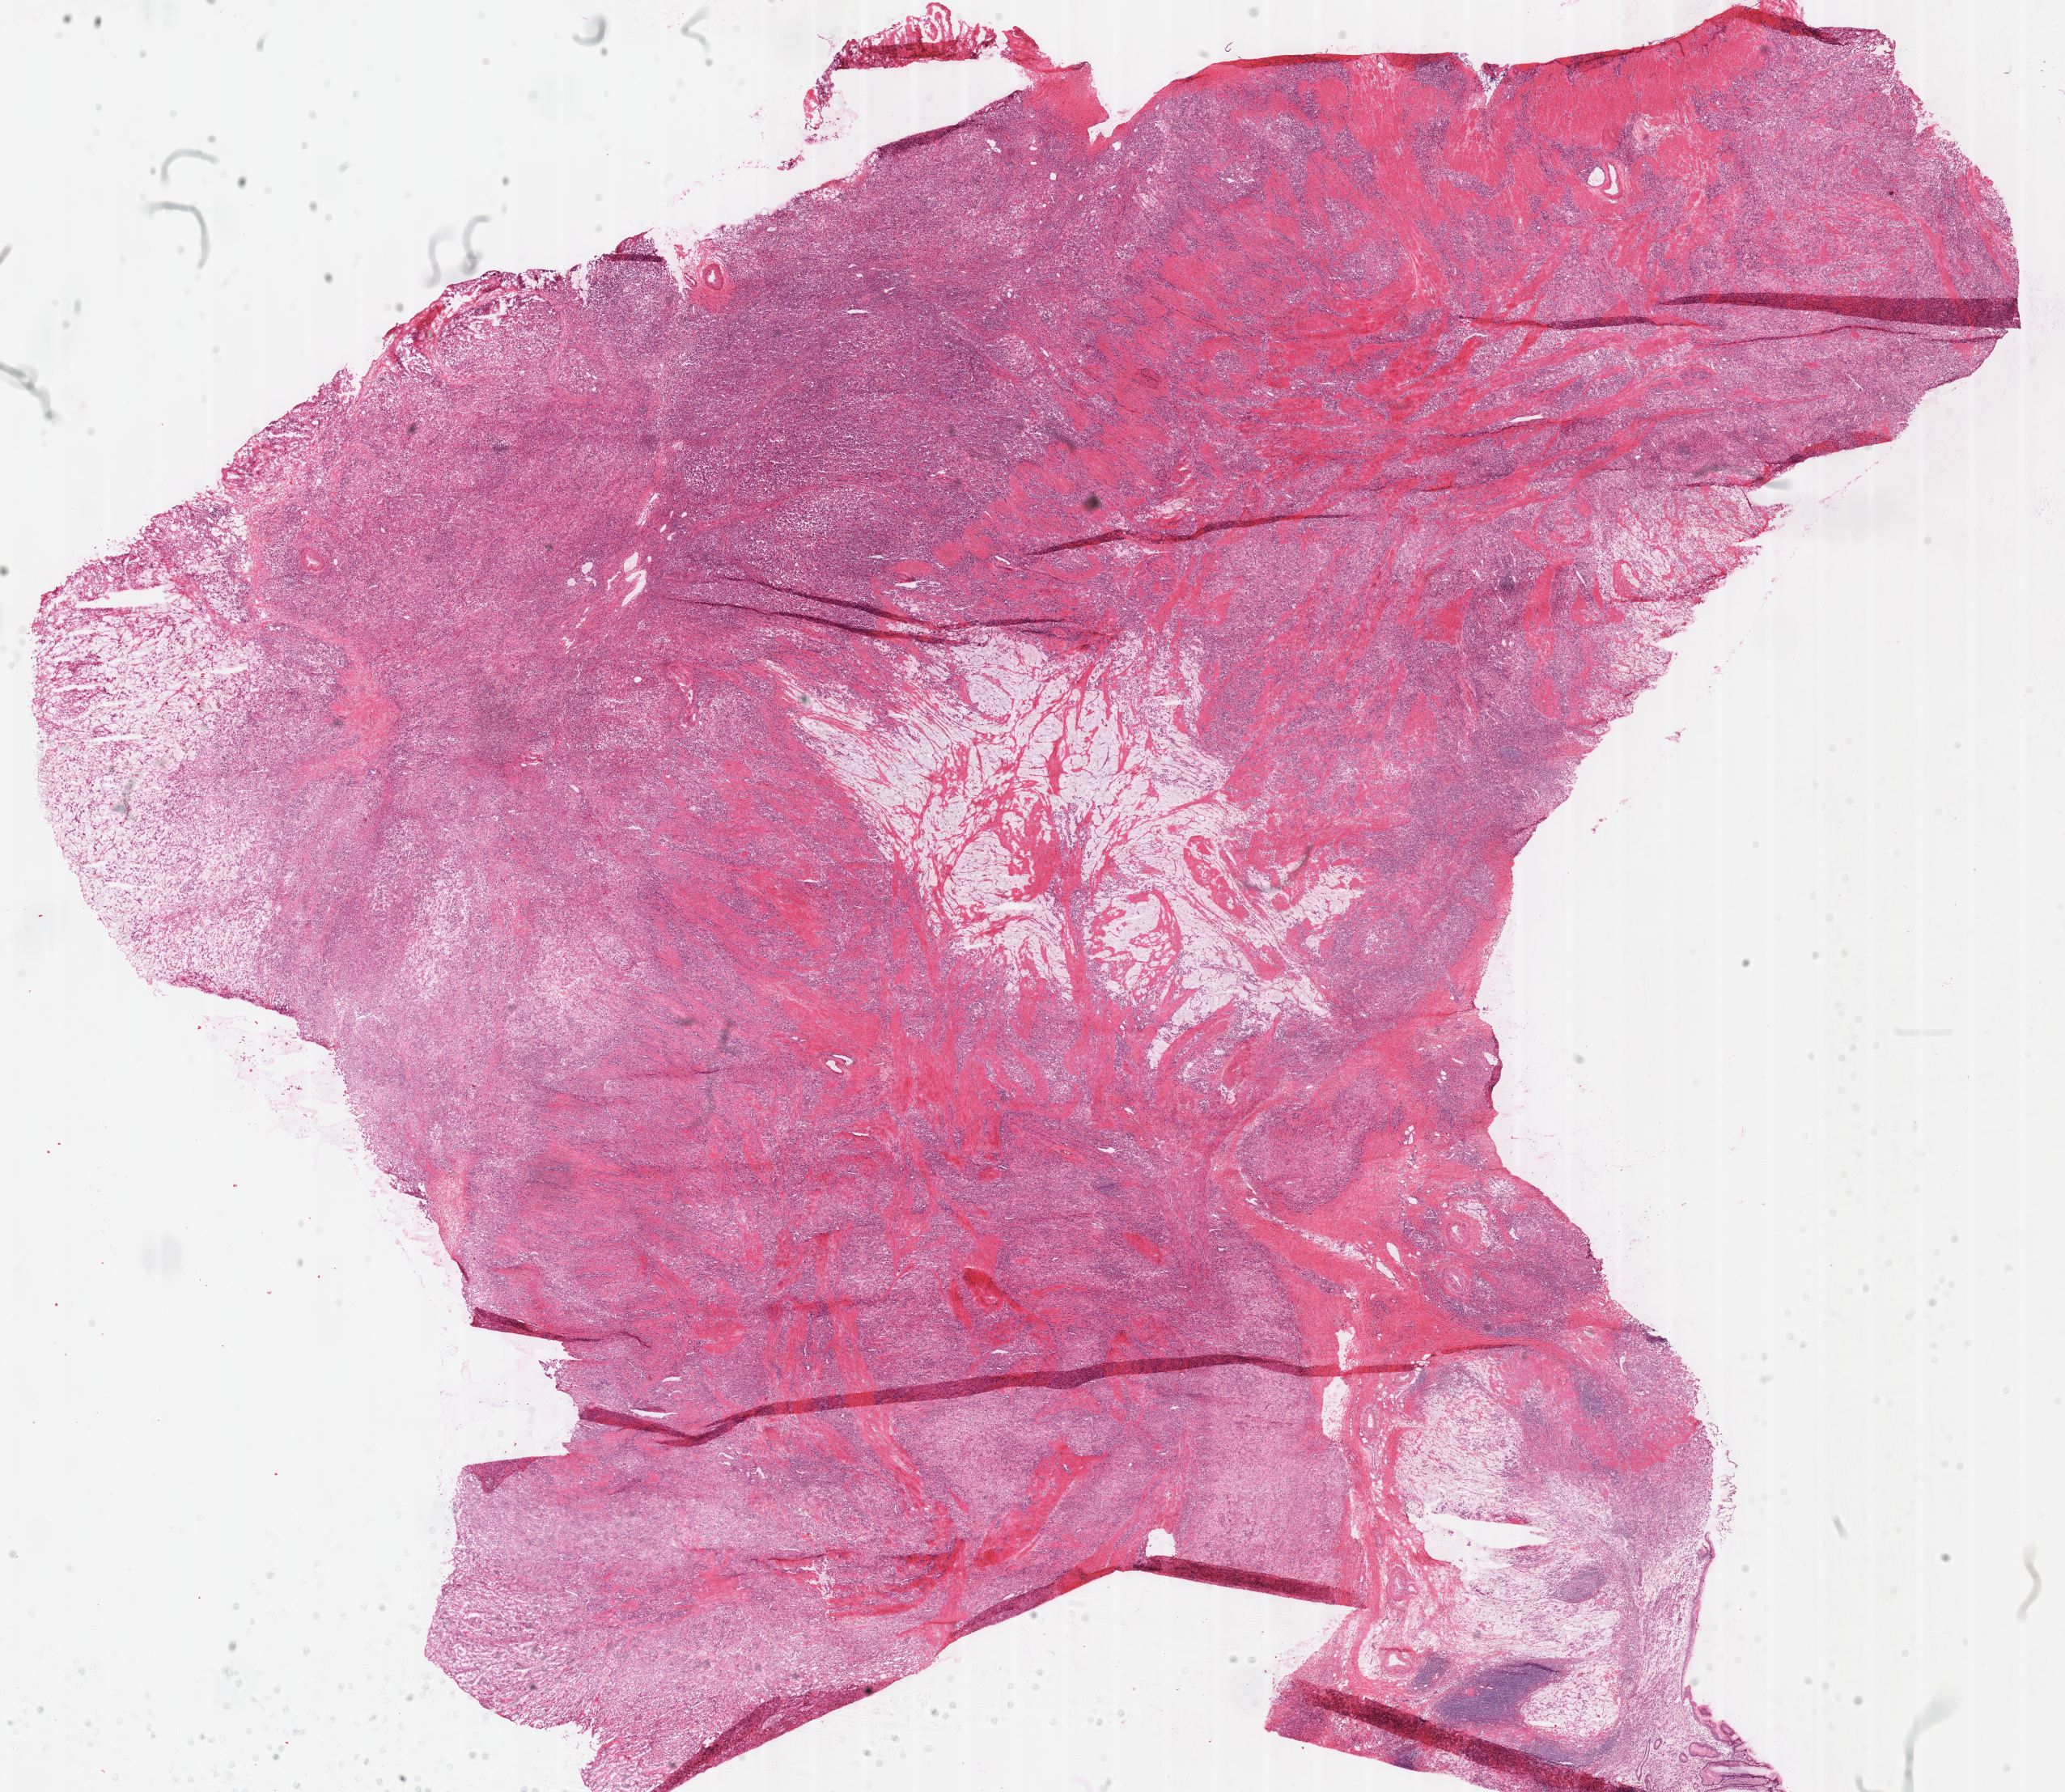
Whole-slide histology image, Hematoxylin and eosin (H&E) stained — shown as a low-resolution overview of the whole scanned area (about 20.1 x 17.4 mm, slide scanned at 40x). Frozen section from the top of the tissue portion. Sample: primary tumour, stomach. Patient: male, age at initial diagnosis 64 years. Histologic grade: G3 (poorly differentiated). Slide review estimates, as recorded: tumour cells 74%, tumour nuclei 75%, normal cells 3%, stromal cells 15%, necrosis 8%.
Lymph nodes positive (case pathology): 9 of 15 examined. AJCC pathologic stage: IIIB (7th edition). Diagnosis: Adenocarcinoma, NOS.